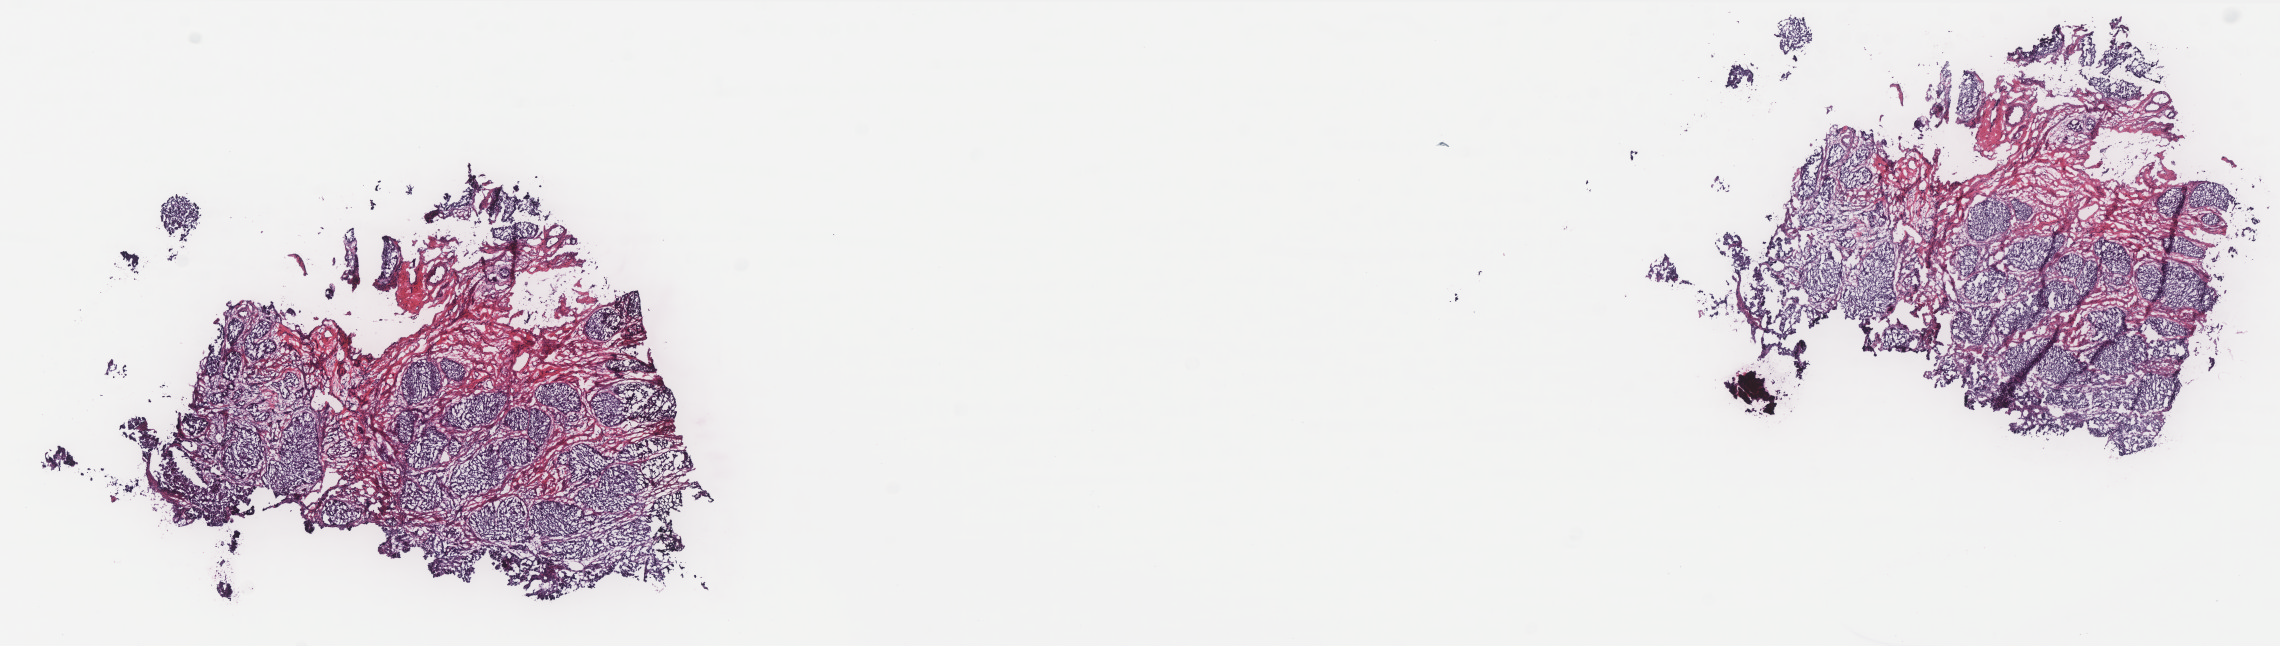
H&E whole-slide image — whole scanned area (about 18.3 x 5.2 mm, slide scanned at 40x) shown as a low-resolution overview, frozen section from the bottom of the tissue portion, cervix, primary tumour sample. Female patient; age at initial diagnosis 45 years. Histologic grade: G3 (poorly differentiated). Slide review estimates, as recorded: tumour cells 80%, tumour nuclei 70%, normal cells 0%, stromal cells 20%, necrosis 0%. Infiltration values recorded for this section: lymphocyte infiltration 0%, monocyte infiltration 0%, neutrophil infiltration 0%.
Diagnosis: Squamous cell carcinoma, NOS (cervix uteri). Lymph nodes positive (case pathology): 1 of 16 examined.